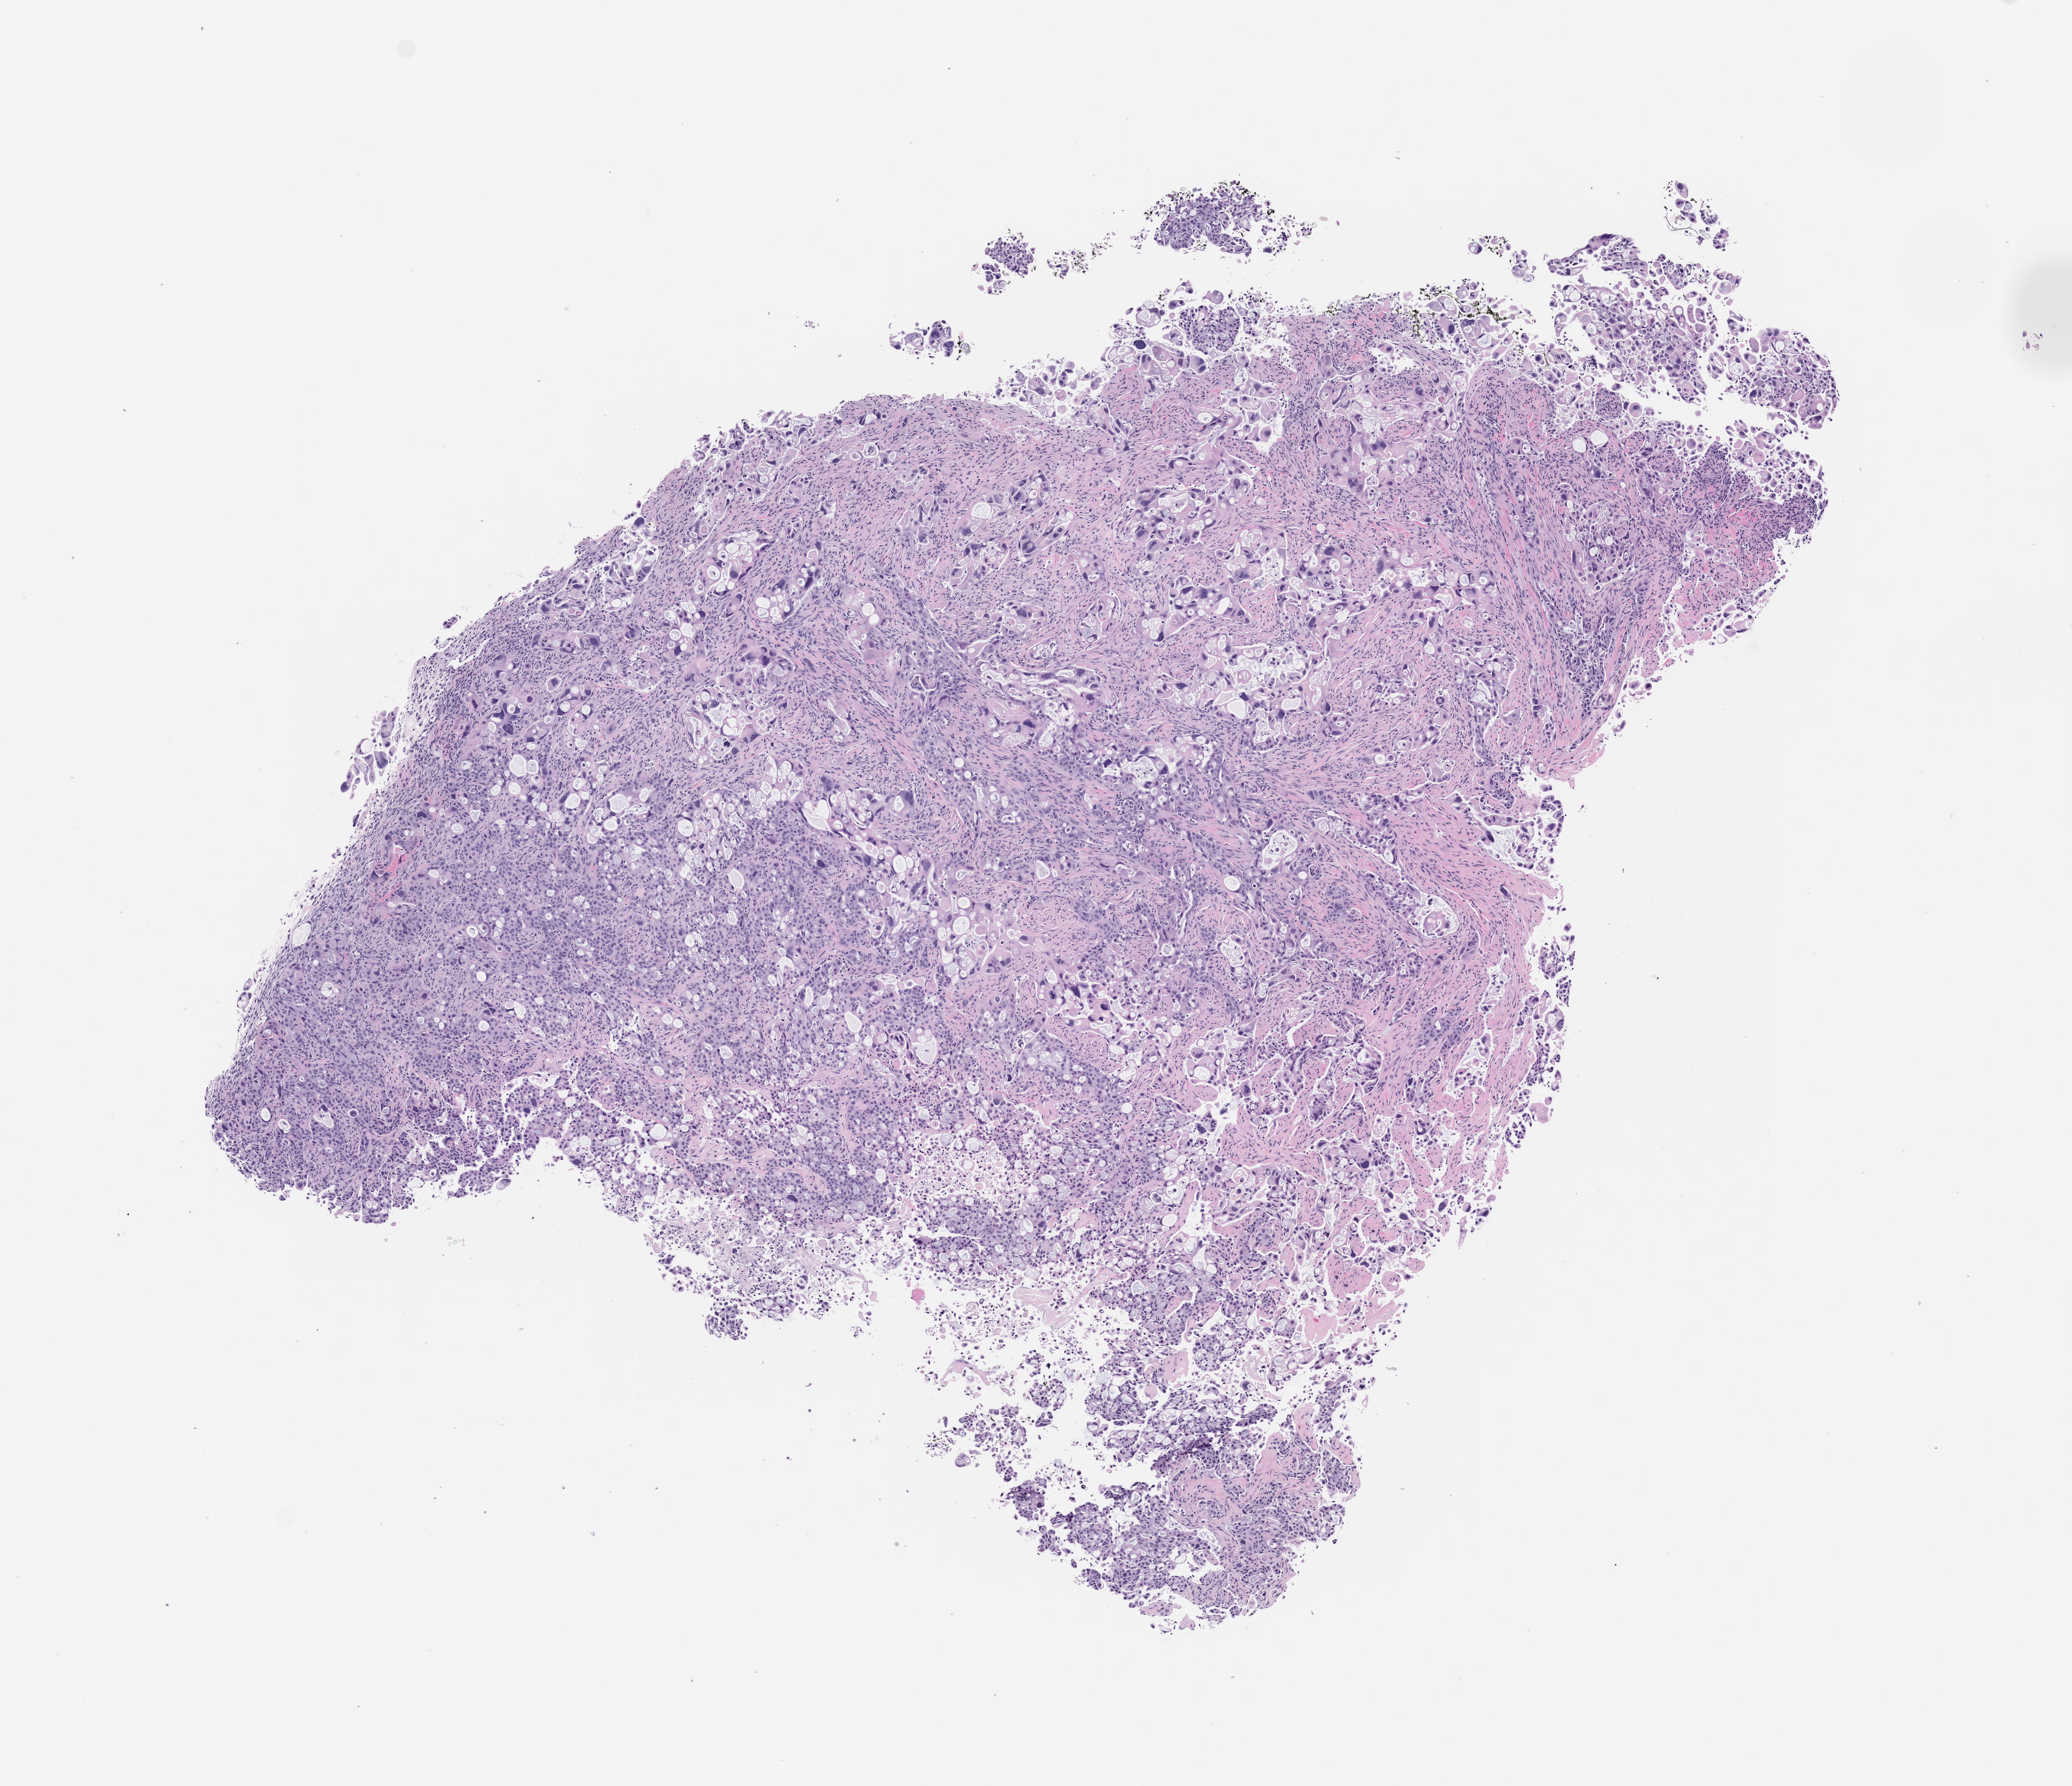
Whole-slide image, haematoxylin and eosin: patient-derived xenograft (human tumor grown in a mouse), passage 2, whole scanned area (about 7.0 x 6.0 mm) shown as a low-resolution overview; formalin-fixed paraffin-embedded section; originating tumor site category: pancreas.
• originating patient diagnosis: Pancreatic Adenocarcinoma